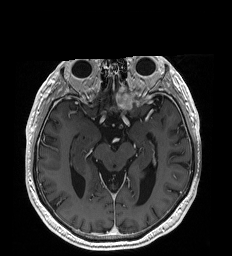
Brain MRI from a brain-tumour surgery series, one axial slice; position 117 of 192 along the scan axis; T1-weighted post-contrast; 1 mm slice thickness; 232 × 256 image matrix, field of view 227 × 250 mm. Case-level facts recorded for this patient, not image findings: histopathology: Glioblastoma; WHO grade: 4; IDH mutation: no.
Structures marked on this image (expert manual segmentation):
- tumour: bounding box <115,87,133,110> (left, top, right, bottom; pixels)